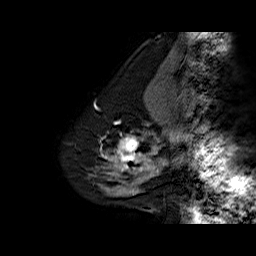
Breast MRI (dynamic contrast-enhanced), one sagittal slice. Position 15 of 60 along the scan axis. Dynamic contrast-enhanced series, time point 2 of 6 at this slice position (early post-contrast). 1.5 T. TE 6.3 ms, TR 32.5 ms. 4 mm slice thickness. 256 × 256 image matrix. Female patient. Case-level facts recorded for this patient, not image findings: setting: breast cancer imaged before/during neoadjuvant chemotherapy; receptor status: triple-negative.
Outlined on this slice (semi-automatically segmented with operator editing):
- analysis volume of interest (the breast-tissue region the enhancement analysis was run in; not a lesion): bounding box [x1, y1, x2, y2] px = [108, 131, 154, 177]
- tumour enhancement mask (voxels above the 100 % enhancement threshold inside the analysis volume of interest): [108, 136, 154, 177]